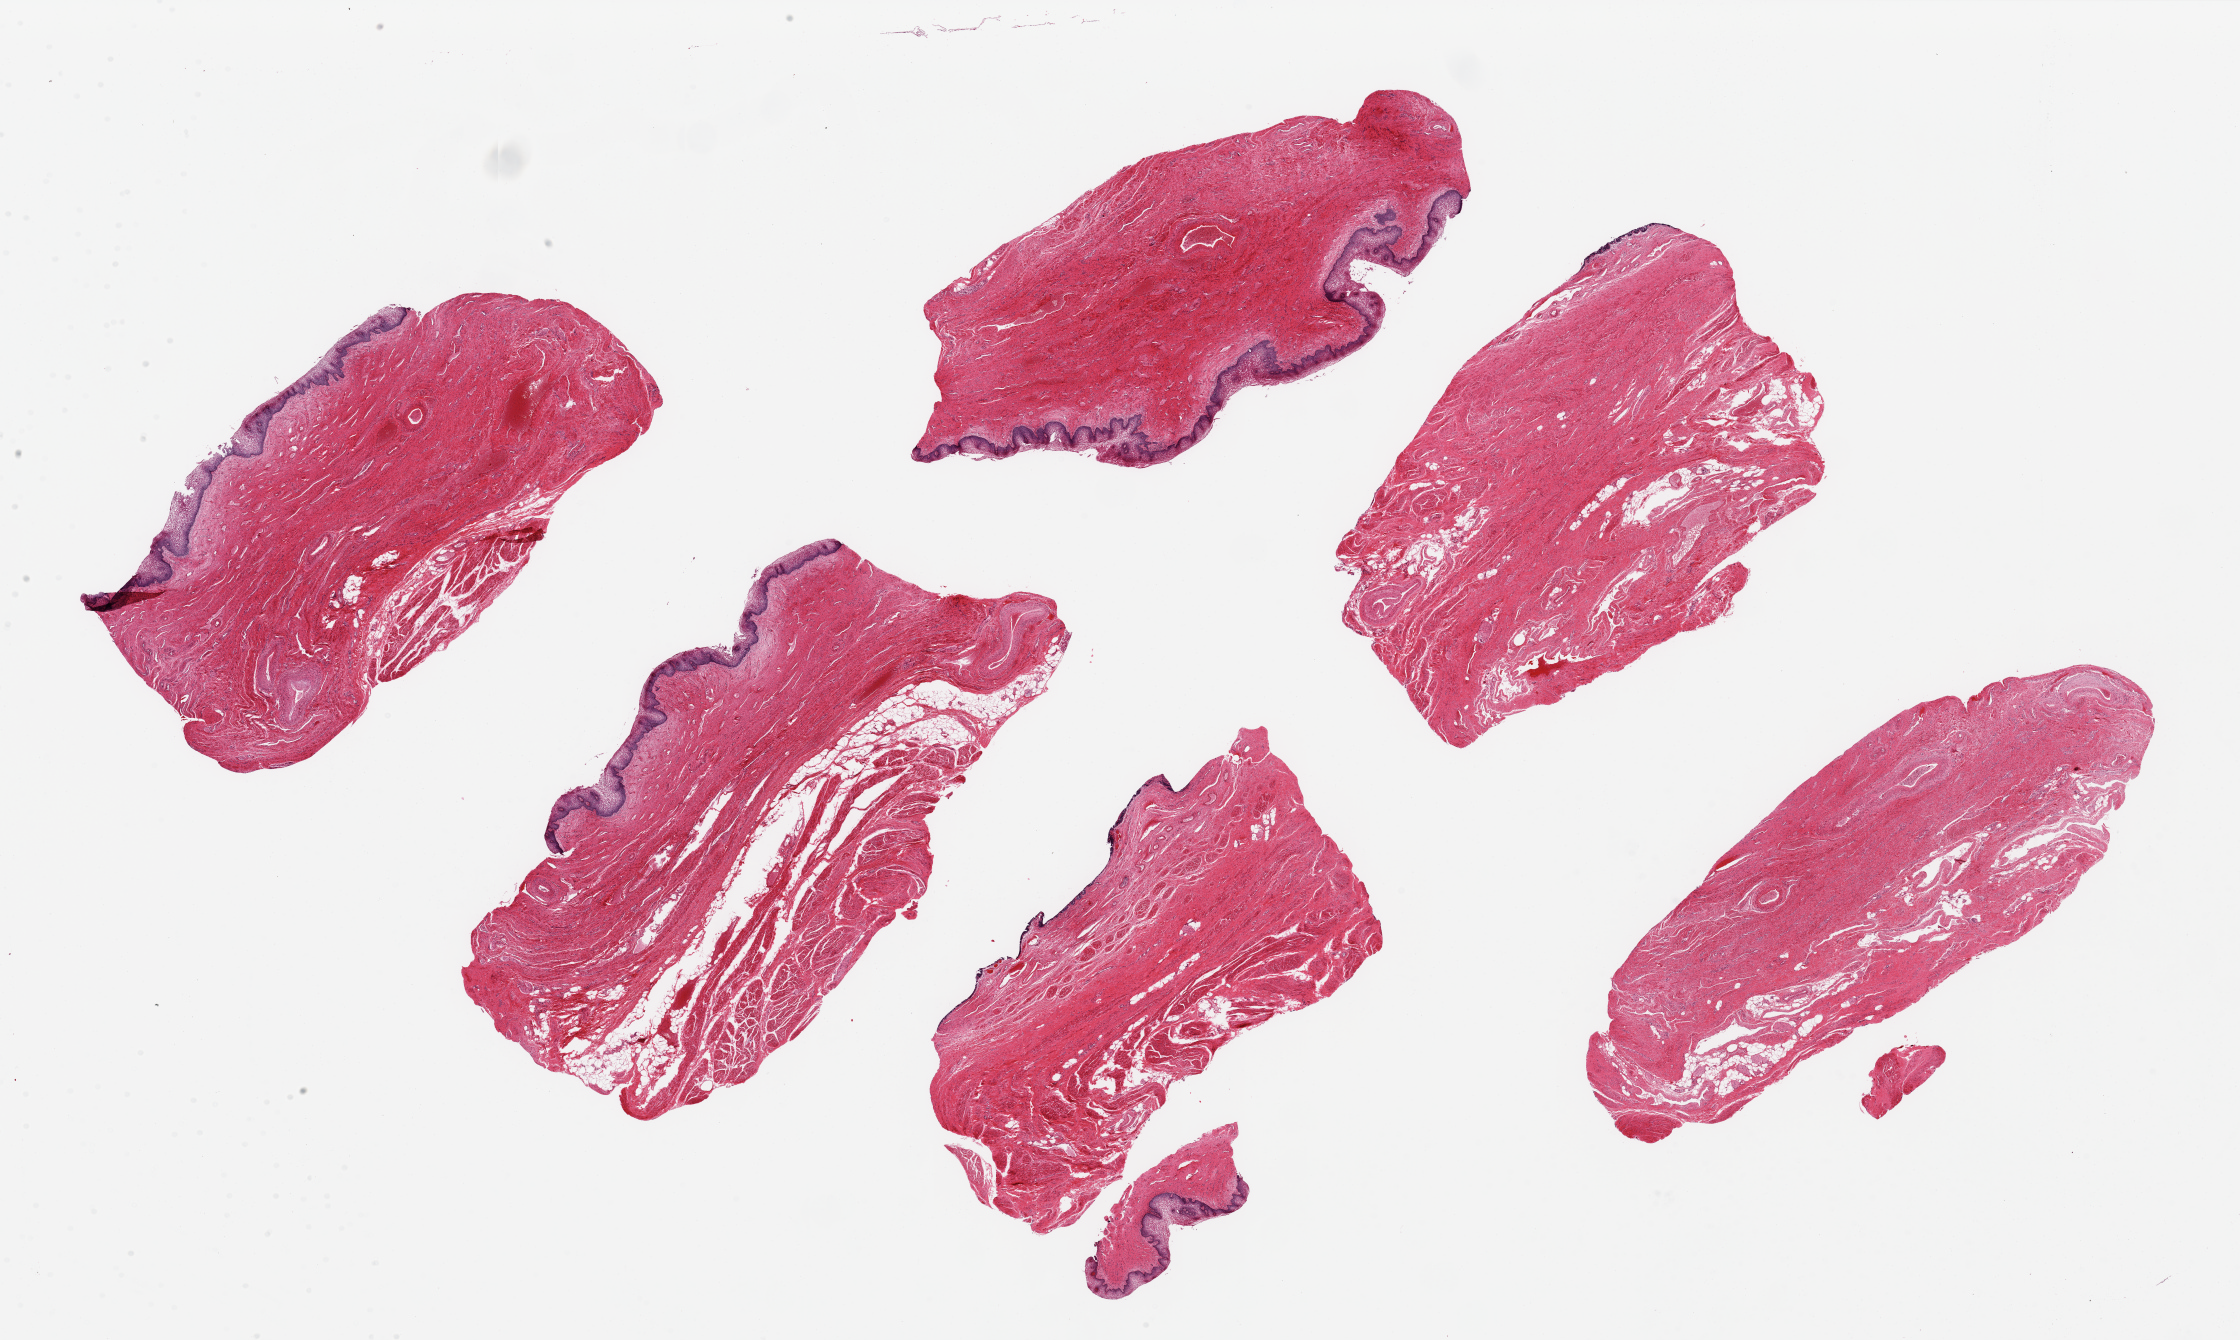
Haematoxylin and eosin whole-slide image, brightfield, a low-resolution overview of the entire scanned area, about 35.4 x 21.2 mm (from a 20x scan). PAXgene-fixed, paraffin-embedded tissue. Section of vagina (target tissue). Donor tissue sample. Donor sex: female.
- review note (as recorded): 6 ~9x4.5mm pieces. Squamous mucosa visible on 3/6, ~5% of thickness